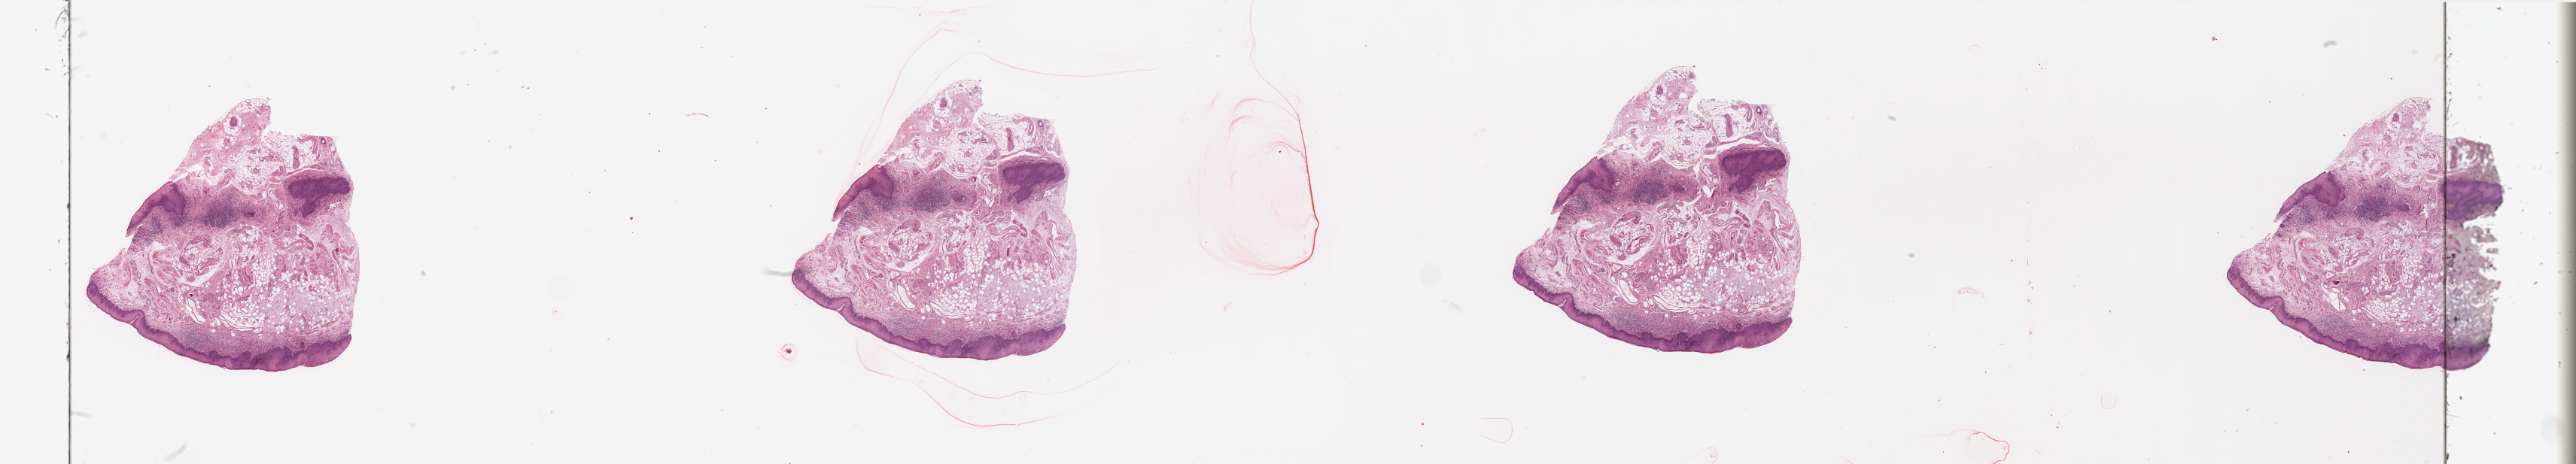
Digitized Hematoxylin and eosin (H&E) stained tissue section (whole slide), whole scanned area (about 54.1 x 9.8 mm, slide scanned at 20x) shown as a low-resolution overview. Normal (non-tumour) tissue sample, sampled site: larynx. 68-year-old male patient.
- this section: normal (non-tumour) tissue from the same patient
- patient diagnosis: Squamous cell carcinoma, NOS (larynx, NOS)